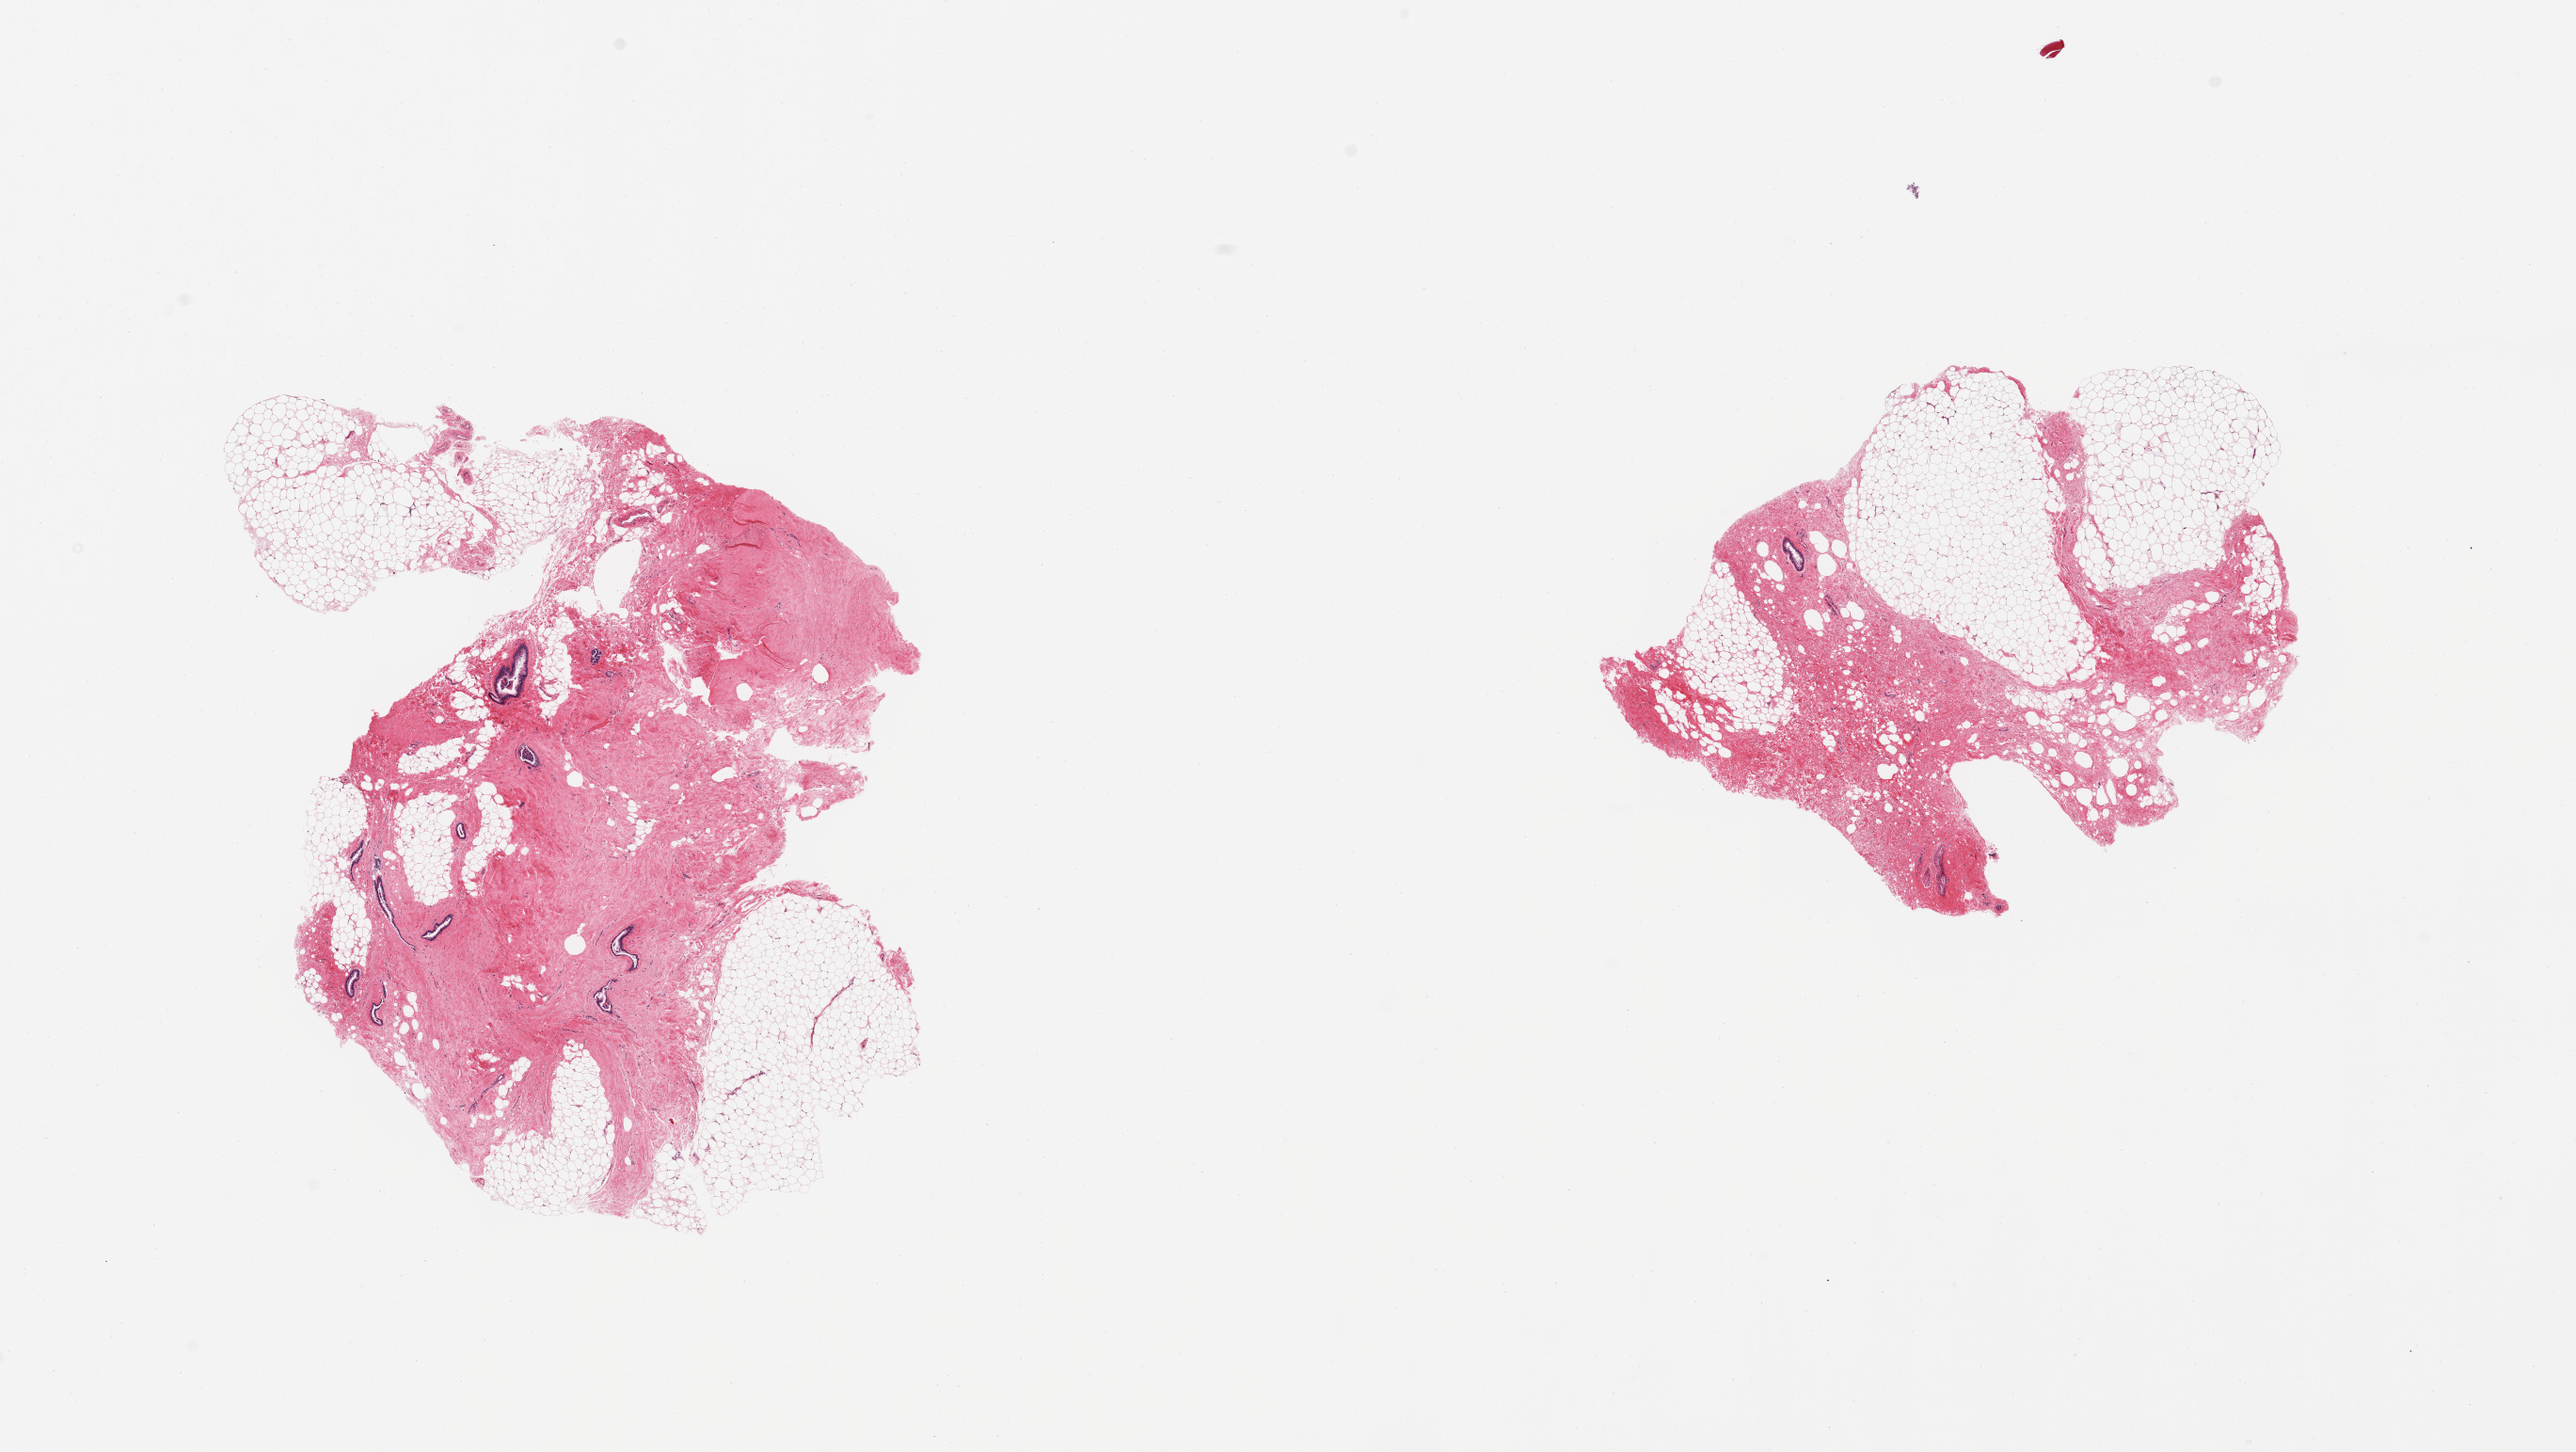
Whole-slide image, H&E stain, a low-resolution overview of the entire scanned area, about 21.7 x 12.2 mm (acquisition: 20x scan), PAXgene-fixed paraffin-embedded (PFPE) section, target tissue: breast, tissue donor sample. Male donor.
Reviewer comment on this tissue sample: 2 pieces, mainly fibroadipose tisssue; a few ductal elements noted.